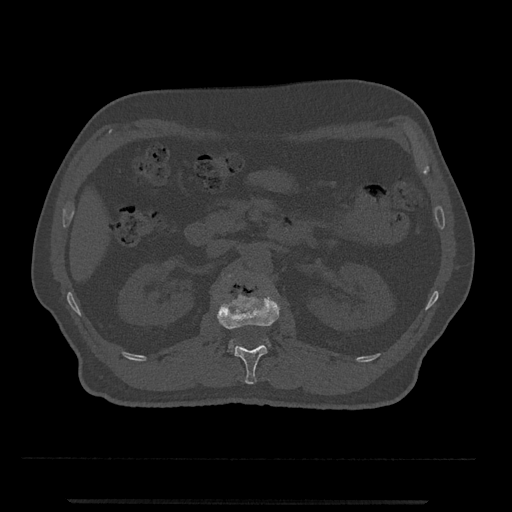
CT including the spine, one axial slice. Position 312 of 797 along the scan axis. Reconstruction kernel Br40s/3. Bone window (W 1800 / L 400 HU). 512 × 512 image matrix, field of view 419 × 419 mm. Patient: male, 63 years. From the clinical record (not read from this slice): primary cancer: prostate.
Outlined on this slice (semi-automatically segmented with operator editing):
- L1 vertebra: bounding box (x1, y1, x2, y2) in pixels: (217, 292, 280, 384)
- L2 vertebra: (227, 274, 270, 350)